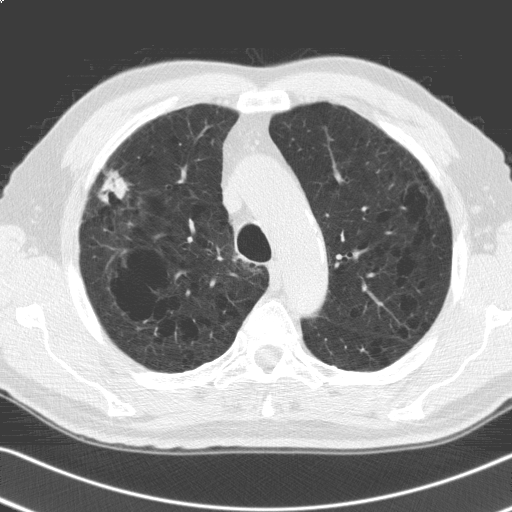
Chest CT (low-dose screening protocol), one axial image. Second annual screen. Lung window (W 1500 / L -600 HU). 3.2 mm slice thickness. Standard (soft-tissue) reconstruction kernel (C). Slice 40 of 168 in the series. Male, age 69 years at enrolment. Former smoker at enrolment.
- Expert-annotated lung lesion, bounding box <87,167,132,216> (left, top, right, bottom; pixels).
- The screening reader recorded 6 non-calcified nodules or masses ≥4 mm on this exam (right upper lobe, right upper lobe, right lower lobe, lingula, left lower lobe, left lower lobe); which of them this box marks is not recorded.
- Official screen result: positive, other.
- Later outcome: lung cancer diagnosed 91 days after this screen — adenosquamous carcinoma, right upper lobe, poorly differentiated (G3), stage IV (AJCC 6th edition), 30 mm at pathology.